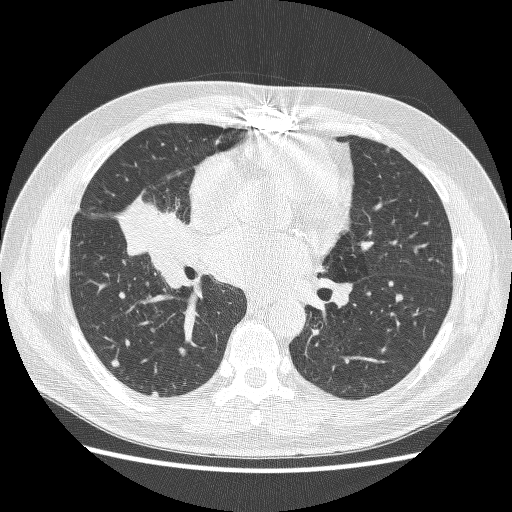
Low-dose screening chest CT, axial slice. First (baseline) screen. Lung window (W 1500 / L -600 HU). Slice 137 of 251 in the series. Male, age 59 years at enrolment.
Expert reader's lesion annotation, bounding box (x1, y1, x2, y2) in pixels: (120, 186, 196, 260). No non-calcified nodule or mass ≥4 mm was recorded by the screening reader at this exam. Lung cancer was diagnosed 24 days after this screen: adenocarcinoma, NOS, right middle lobe, poorly differentiated (G3), stage IV (AJCC 6th edition), 54 mm at pathology.